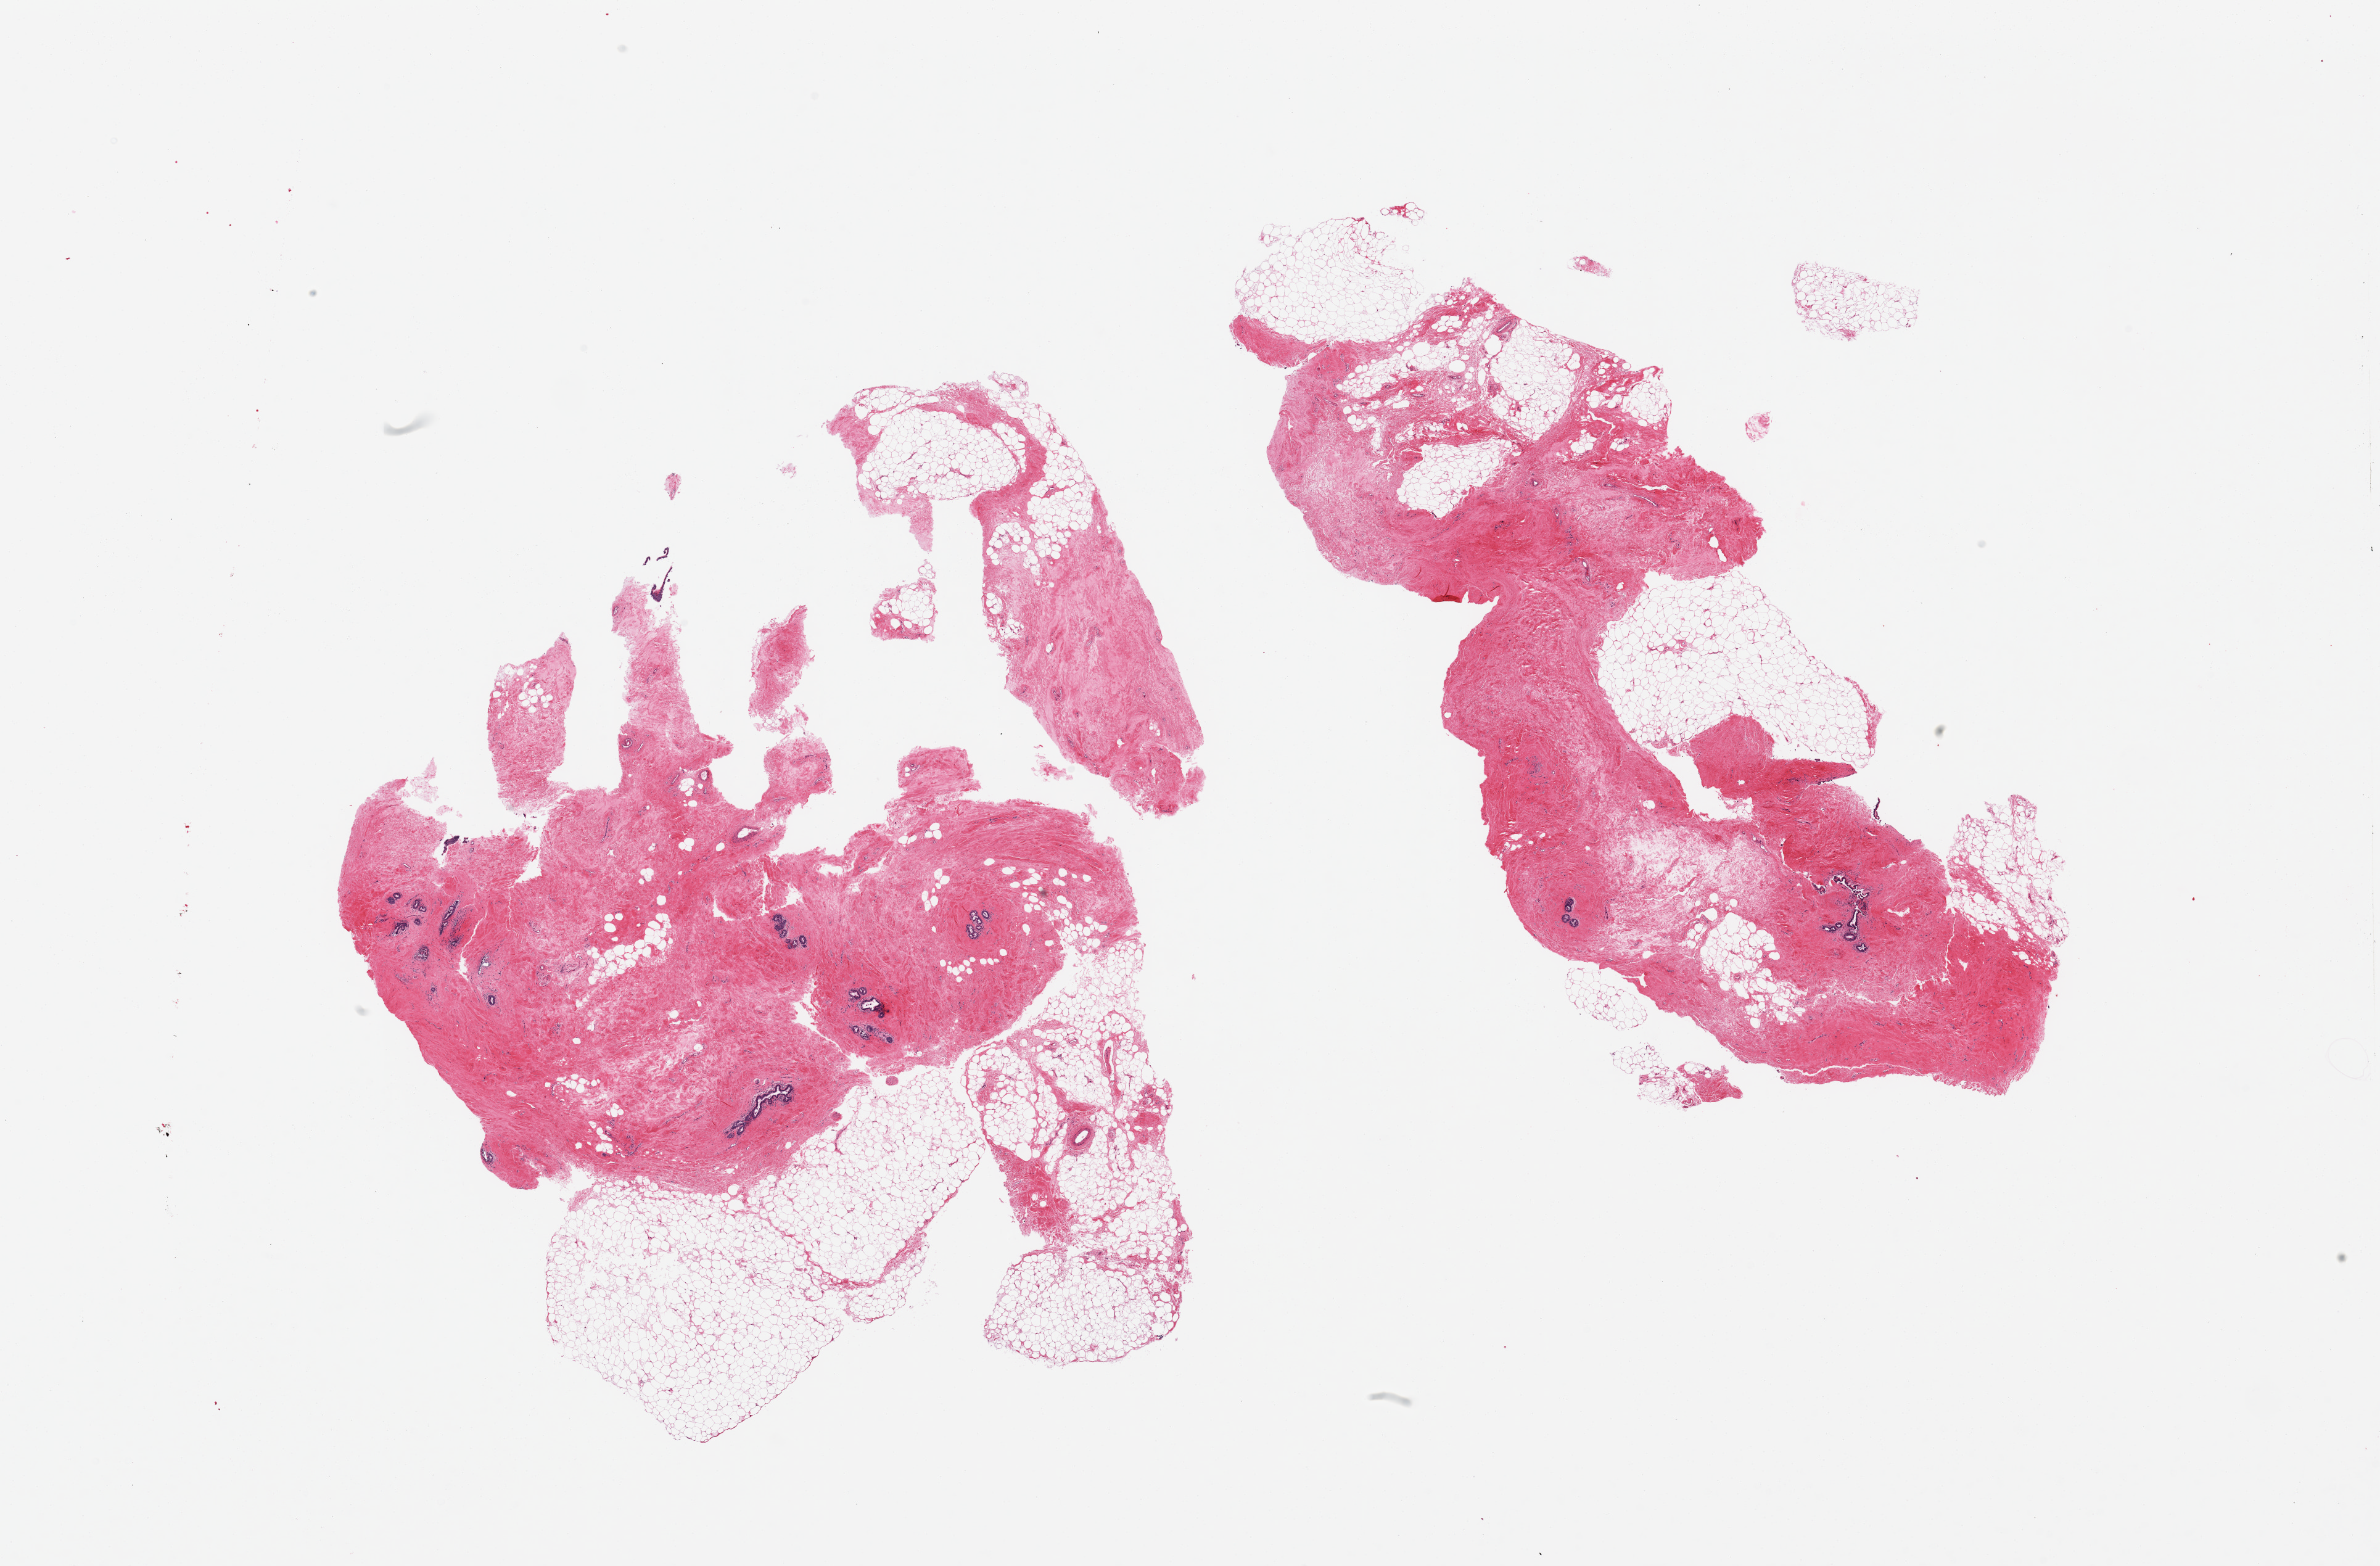
Haematoxylin and eosin whole-slide image — low-resolution overview of the scanned area, about 30.5 x 20.1 mm (slide scanned at 20x). PAXgene-fixed paraffin-embedded (PFPE) section. Sampled site (target tissue): breast. Tissue donor sample. Donor sex: male.
Reviewer comment on this tissue sample: 2 pieces; gynecomastoid stromal and ductal hyperplasia;~50% mature adipose tissue.